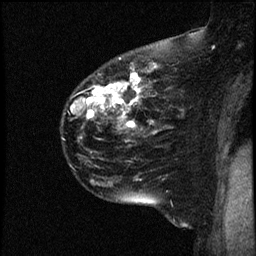
Breast MRI (dynamic contrast-enhanced), one sagittal slice; slice 35 of 44 in the series (ordered by position); dynamic contrast-enhanced study with each time point stored as its own series, time point 2 of 4 at this slice position (early post-contrast, ordered by acquisition time); 1.5 T; TE 4.2 ms, TR 17.7 ms; 2 mm slice thickness; 256 × 256 image matrix. Female patient, age 52 years. From the clinical record (not read from this slice): setting: breast cancer imaged before/during neoadjuvant chemotherapy; receptor status: HR-positive, HER2-negative.
Structures marked on this image (semi-automatically segmented with operator editing):
- analysis volume of interest (the breast-tissue region the enhancement analysis was run in; not a lesion): bounding box [x1, y1, x2, y2] px = [61, 48, 163, 147]
- tumour enhancement mask (voxels above the 100 % enhancement threshold inside the analysis volume of interest): [71, 58, 154, 128]